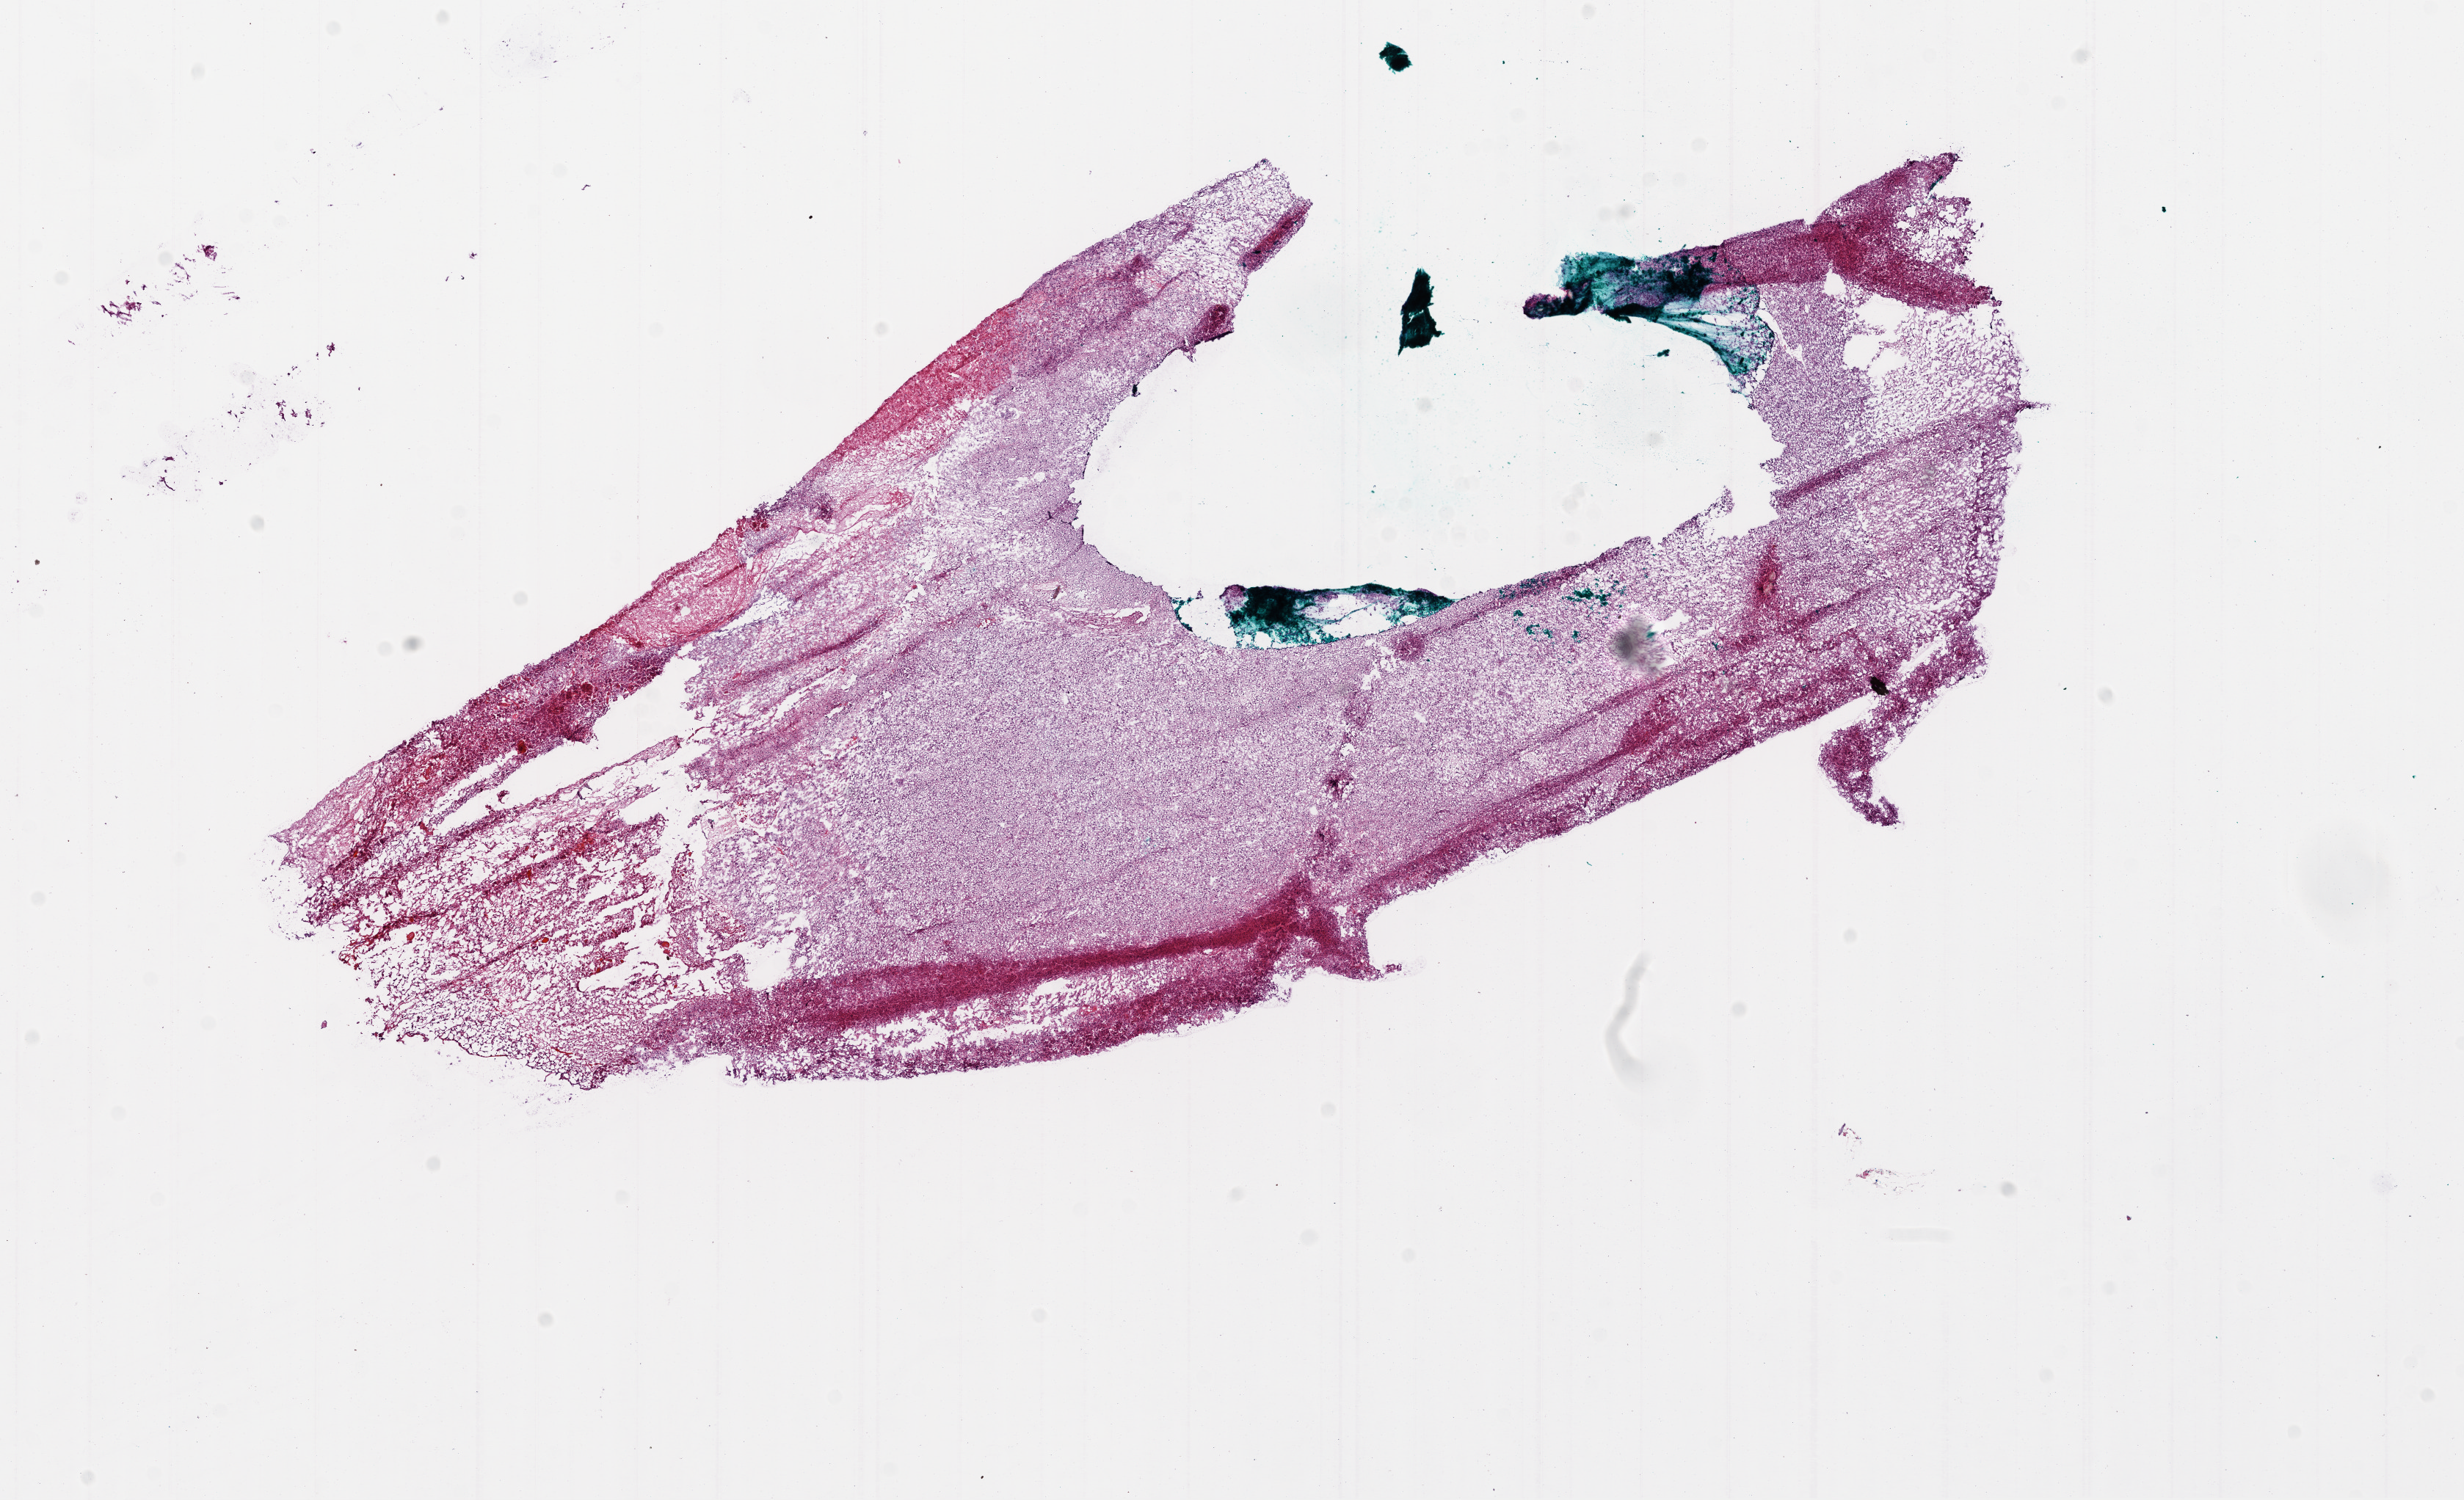
Whole-slide histology image, H&E — low-resolution overview of the scanned area, about 13.5 x 8.2 mm (from a 20x scan); frozen section from the bottom of the tissue portion; sample: primary tumour, brain. Patient: female, age at initial diagnosis 56 years. Slide review estimates, as recorded: tumour cells 75%, tumour nuclei 85%, normal cells 0%, stromal cells 5%, necrosis 25%.
Histologic diagnosis: Glioblastoma.